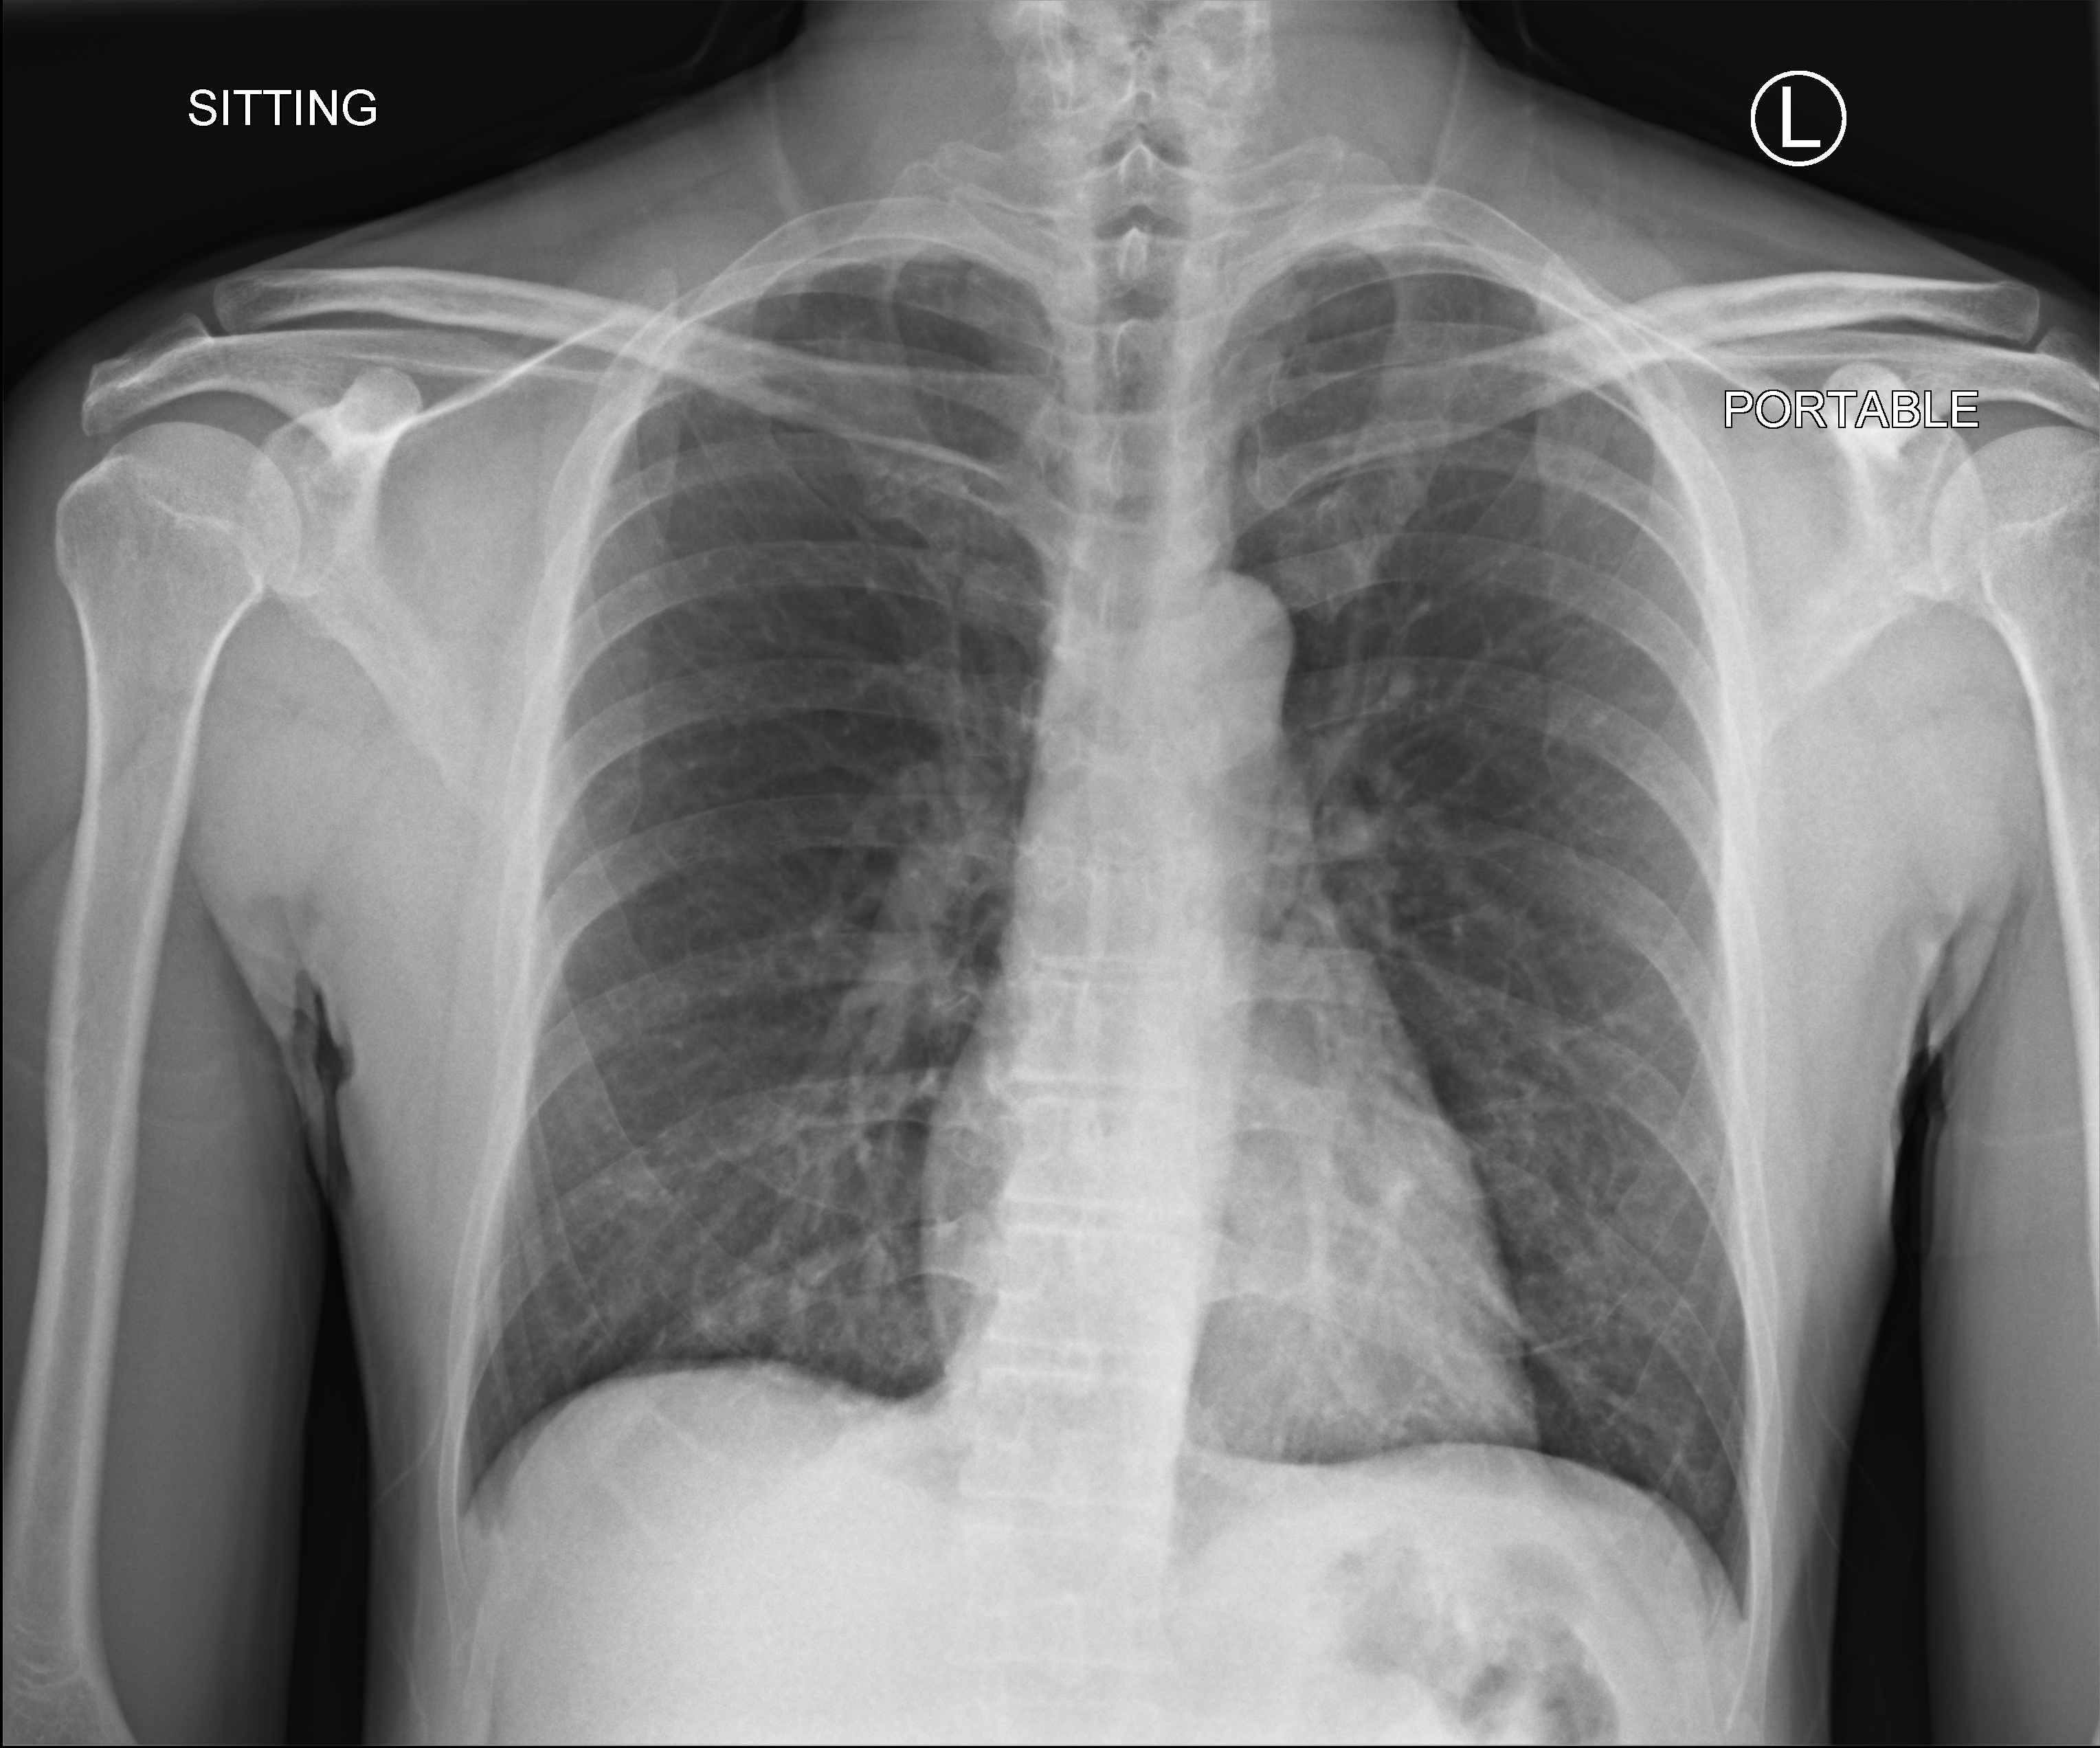
Chest X-ray (portable). Male patient hospitalised with COVID-19, age 18–59 years.
From the hospital-stay record, not from the radiograph (when in the stay this image was taken is not recorded):
- length of hospital stay: 1 day
- mechanically ventilated during this hospital stay: no